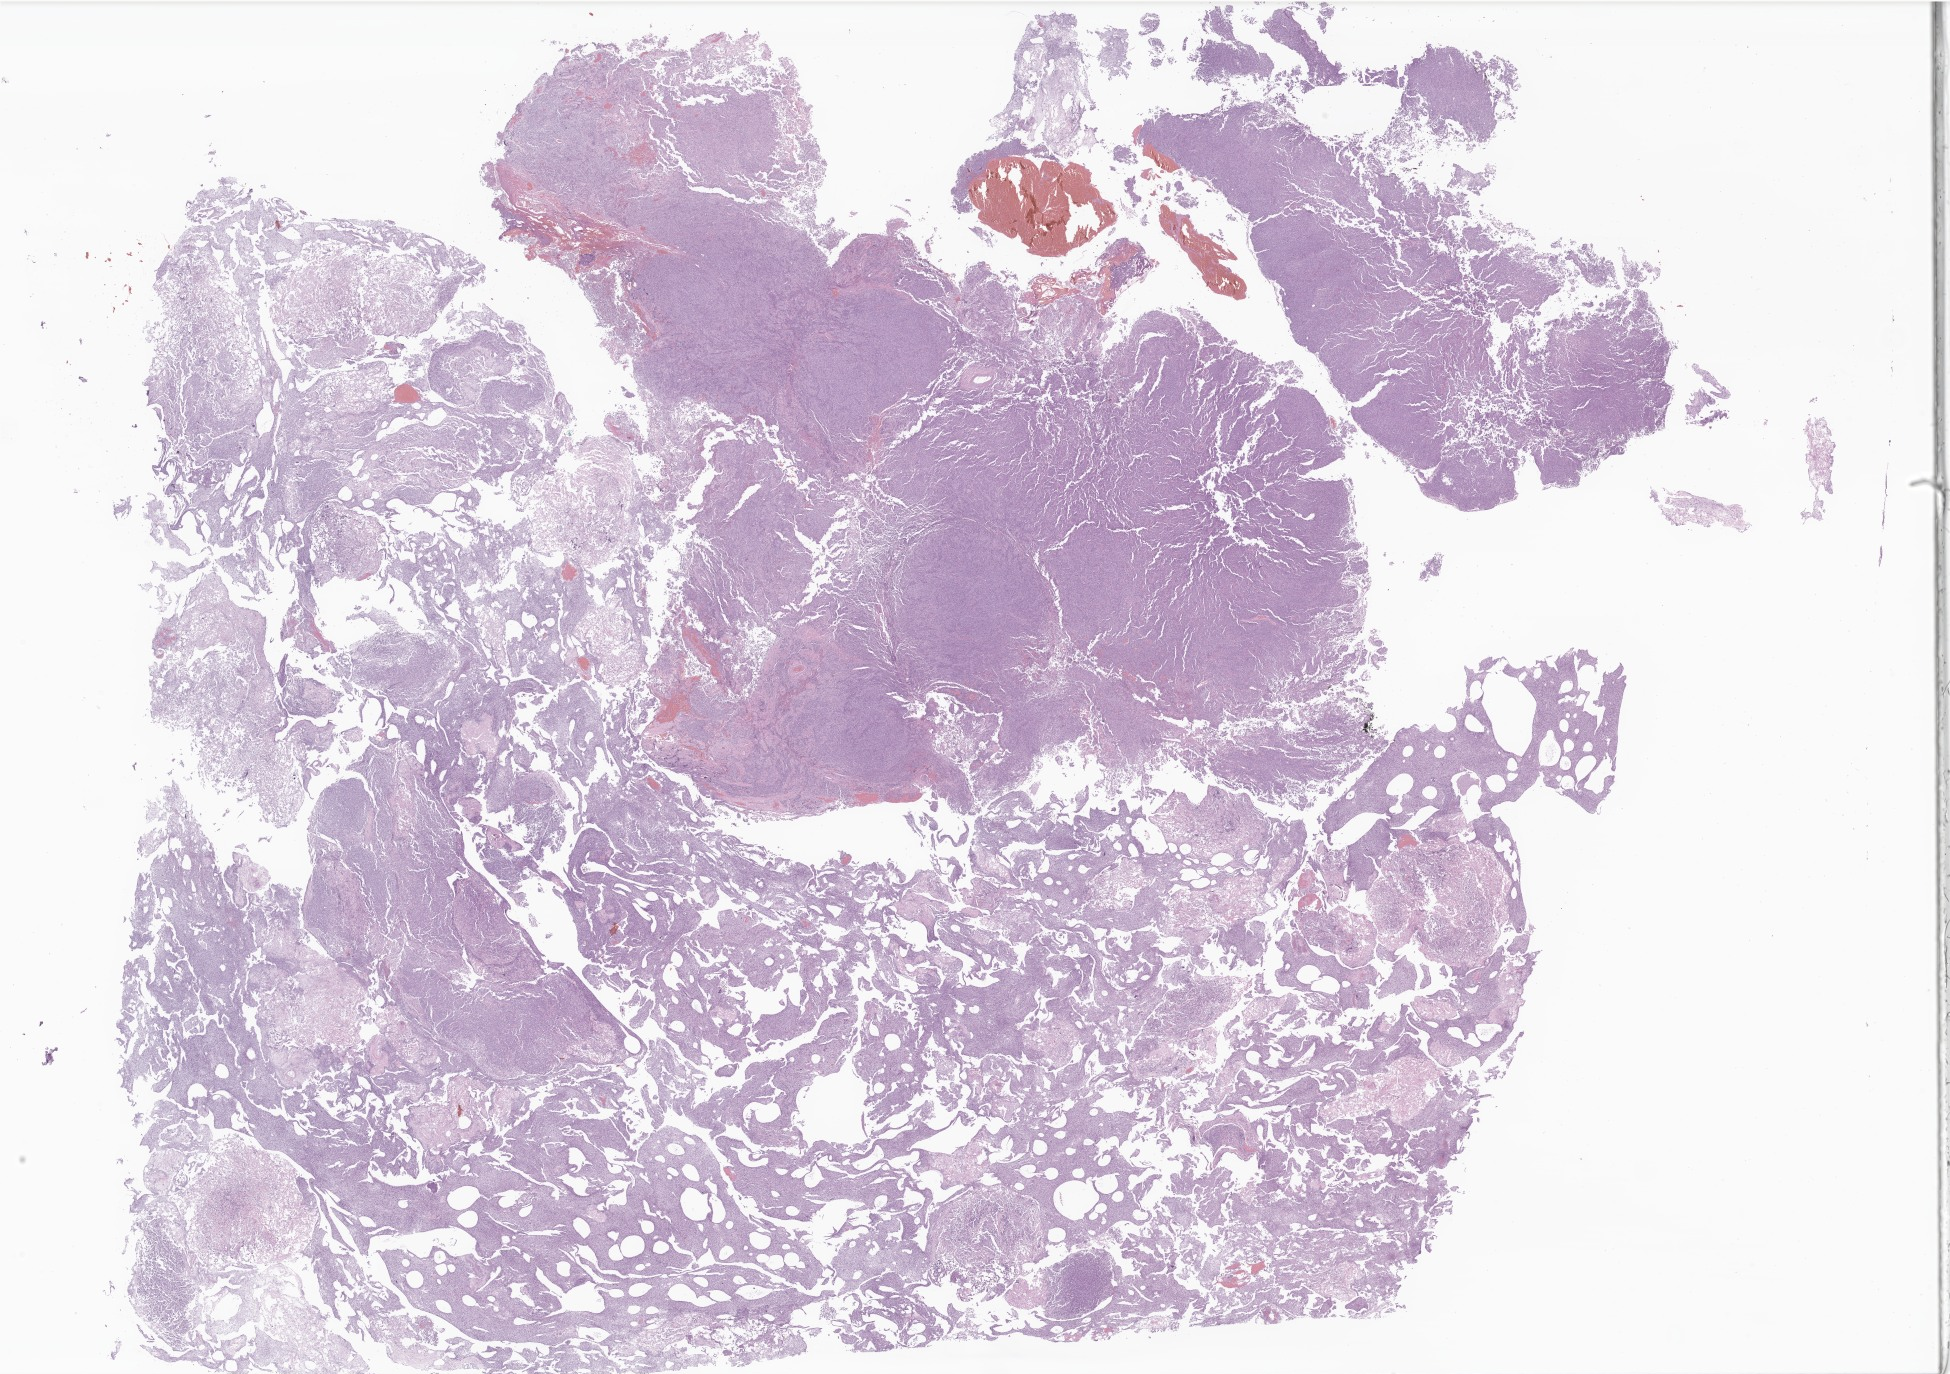
Whole-slide image, haematoxylin and eosin stain of tumor tissue from the brain, low-resolution overview of the scanned area, about 32.9 x 23.2 mm, formalin-fixed, paraffin-embedded (FFPE) tissue. Female patient, age 96 months.
Diagnosis (ICD-O-3 morphology term): Astroblastoma.